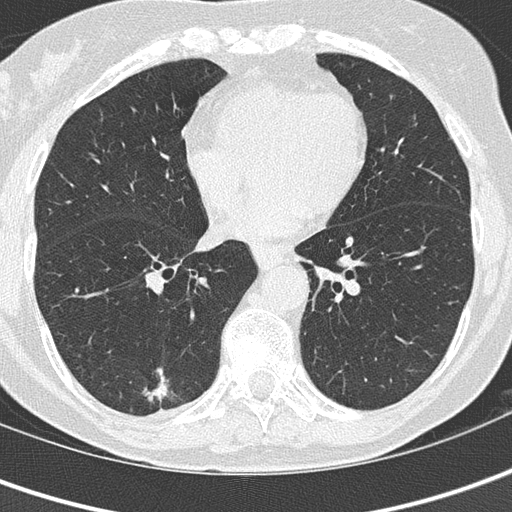
Axial slice from a low-dose chest CT screening exam. Second screening round (one year after baseline). Lung window (W 1500 / L -600 HU). Lung (sharp) reconstruction kernel (B50f). Slice 91 of 152 in the series. Female, age 69 years at enrolment.
Expert-annotated lung lesion, bounding box (x1, y1, x2, y2) in pixels: (122, 363, 183, 422). The screening reader recorded 2 non-calcified nodules or masses ≥4 mm on this exam; which of them this box marks is not recorded. Official screen result: positive, other. Lung cancer was diagnosed 112 days after this screen: adenocarcinoma, NOS, right lower lobe, moderately differentiated (G2), stage IA (AJCC 6th edition), 16 mm at pathology.